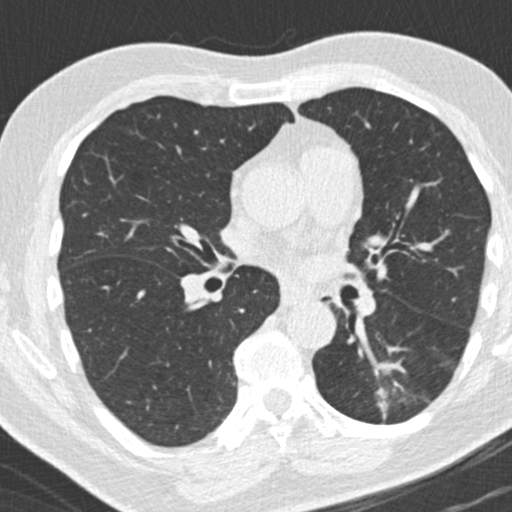
Low-dose screening chest CT, one axial slice; slice 102 of 180 in the series (ordered by position); lung window (W 1500 / L -600 HU); 512 × 512 image matrix, field of view 300 × 300 mm.
Outlined on this slice (expert manual segmentation):
- lesion 1 (tumor, lower lobe of left lung): bounding box [x1, y1, x2, y2] px = [378, 363, 396, 371]